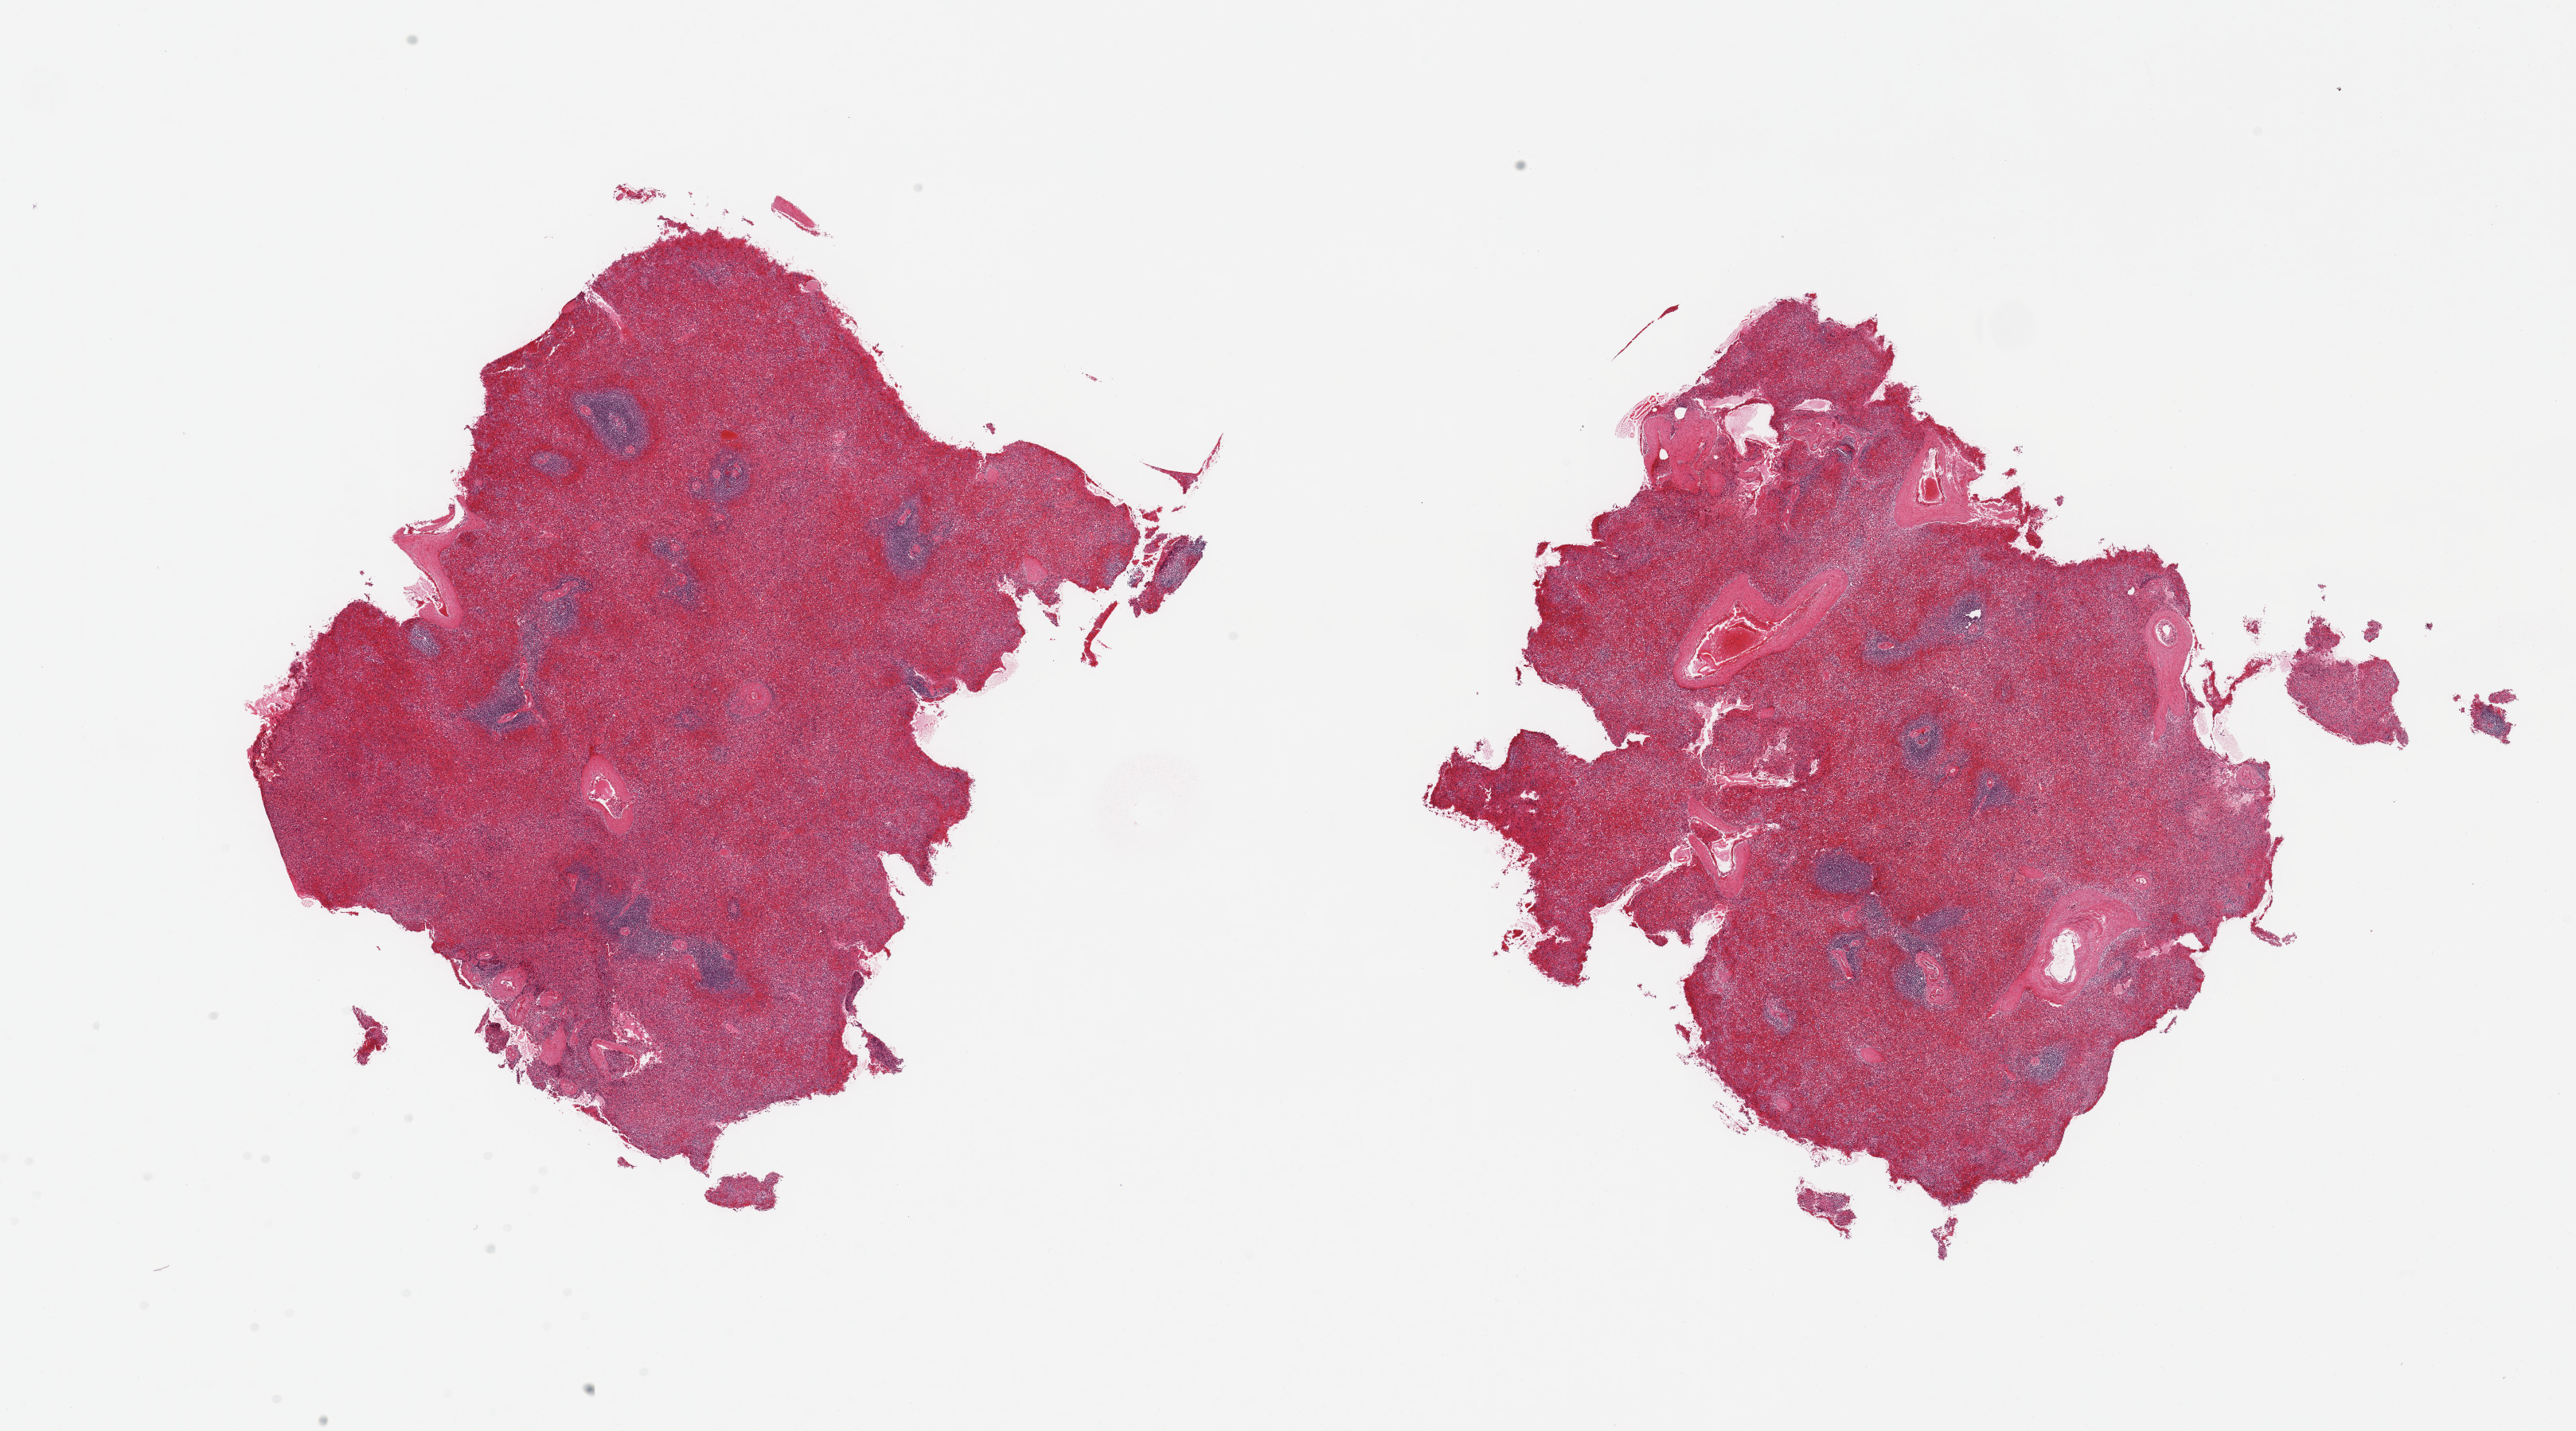
Digitized hematoxylin and eosin (H&E)-stained section, shown as a low-resolution overview of the whole scanned area (about 25.6 x 14.2 mm, slide scanned at 20x). PAXgene-fixed paraffin-embedded (PFPE) section. Sampled site (target tissue): spleen. Donor tissue sample.
Review note (as recorded): 2 pieces, moderate congestion.